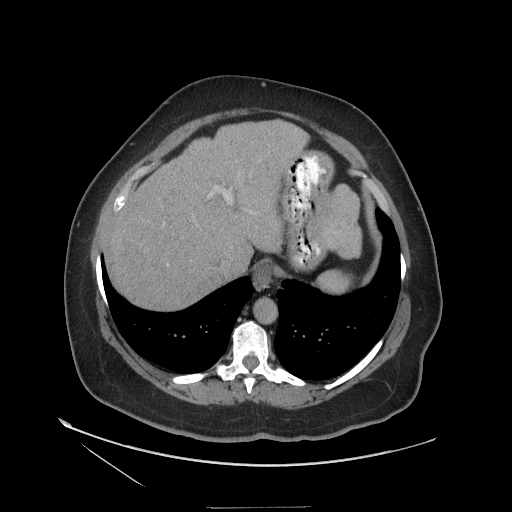
Contrast-enhanced abdominal CT (liver protocol), one axial slice; position 94 of 127 along the scan axis; 140 kVp; soft-tissue window (W 400 / L 40 HU); 2.5 mm slice thickness; 512 × 512 image matrix, field of view 480 × 480 mm. From the clinical record (not read from this slice): diagnosis: hepatocellular carcinoma (patient treated with transarterial chemoembolisation; whether this scan precedes or follows treatment is not stated here); TNM stage (as recorded): Stage-II; Child-Pugh class: A; tumour differentiation: well differentiated.
Structures marked on this image (semi-automatic segmentation, software-assisted and operator-edited):
- abdominal aorta: bounding box [x1, y1, x2, y2] px = [253, 298, 276, 324]
- liver parenchyma outside the tumour (the mass and vessels are separate outlines, so this box may not span the whole liver): [106, 120, 360, 310]
- liver vessels: [117, 187, 231, 210]